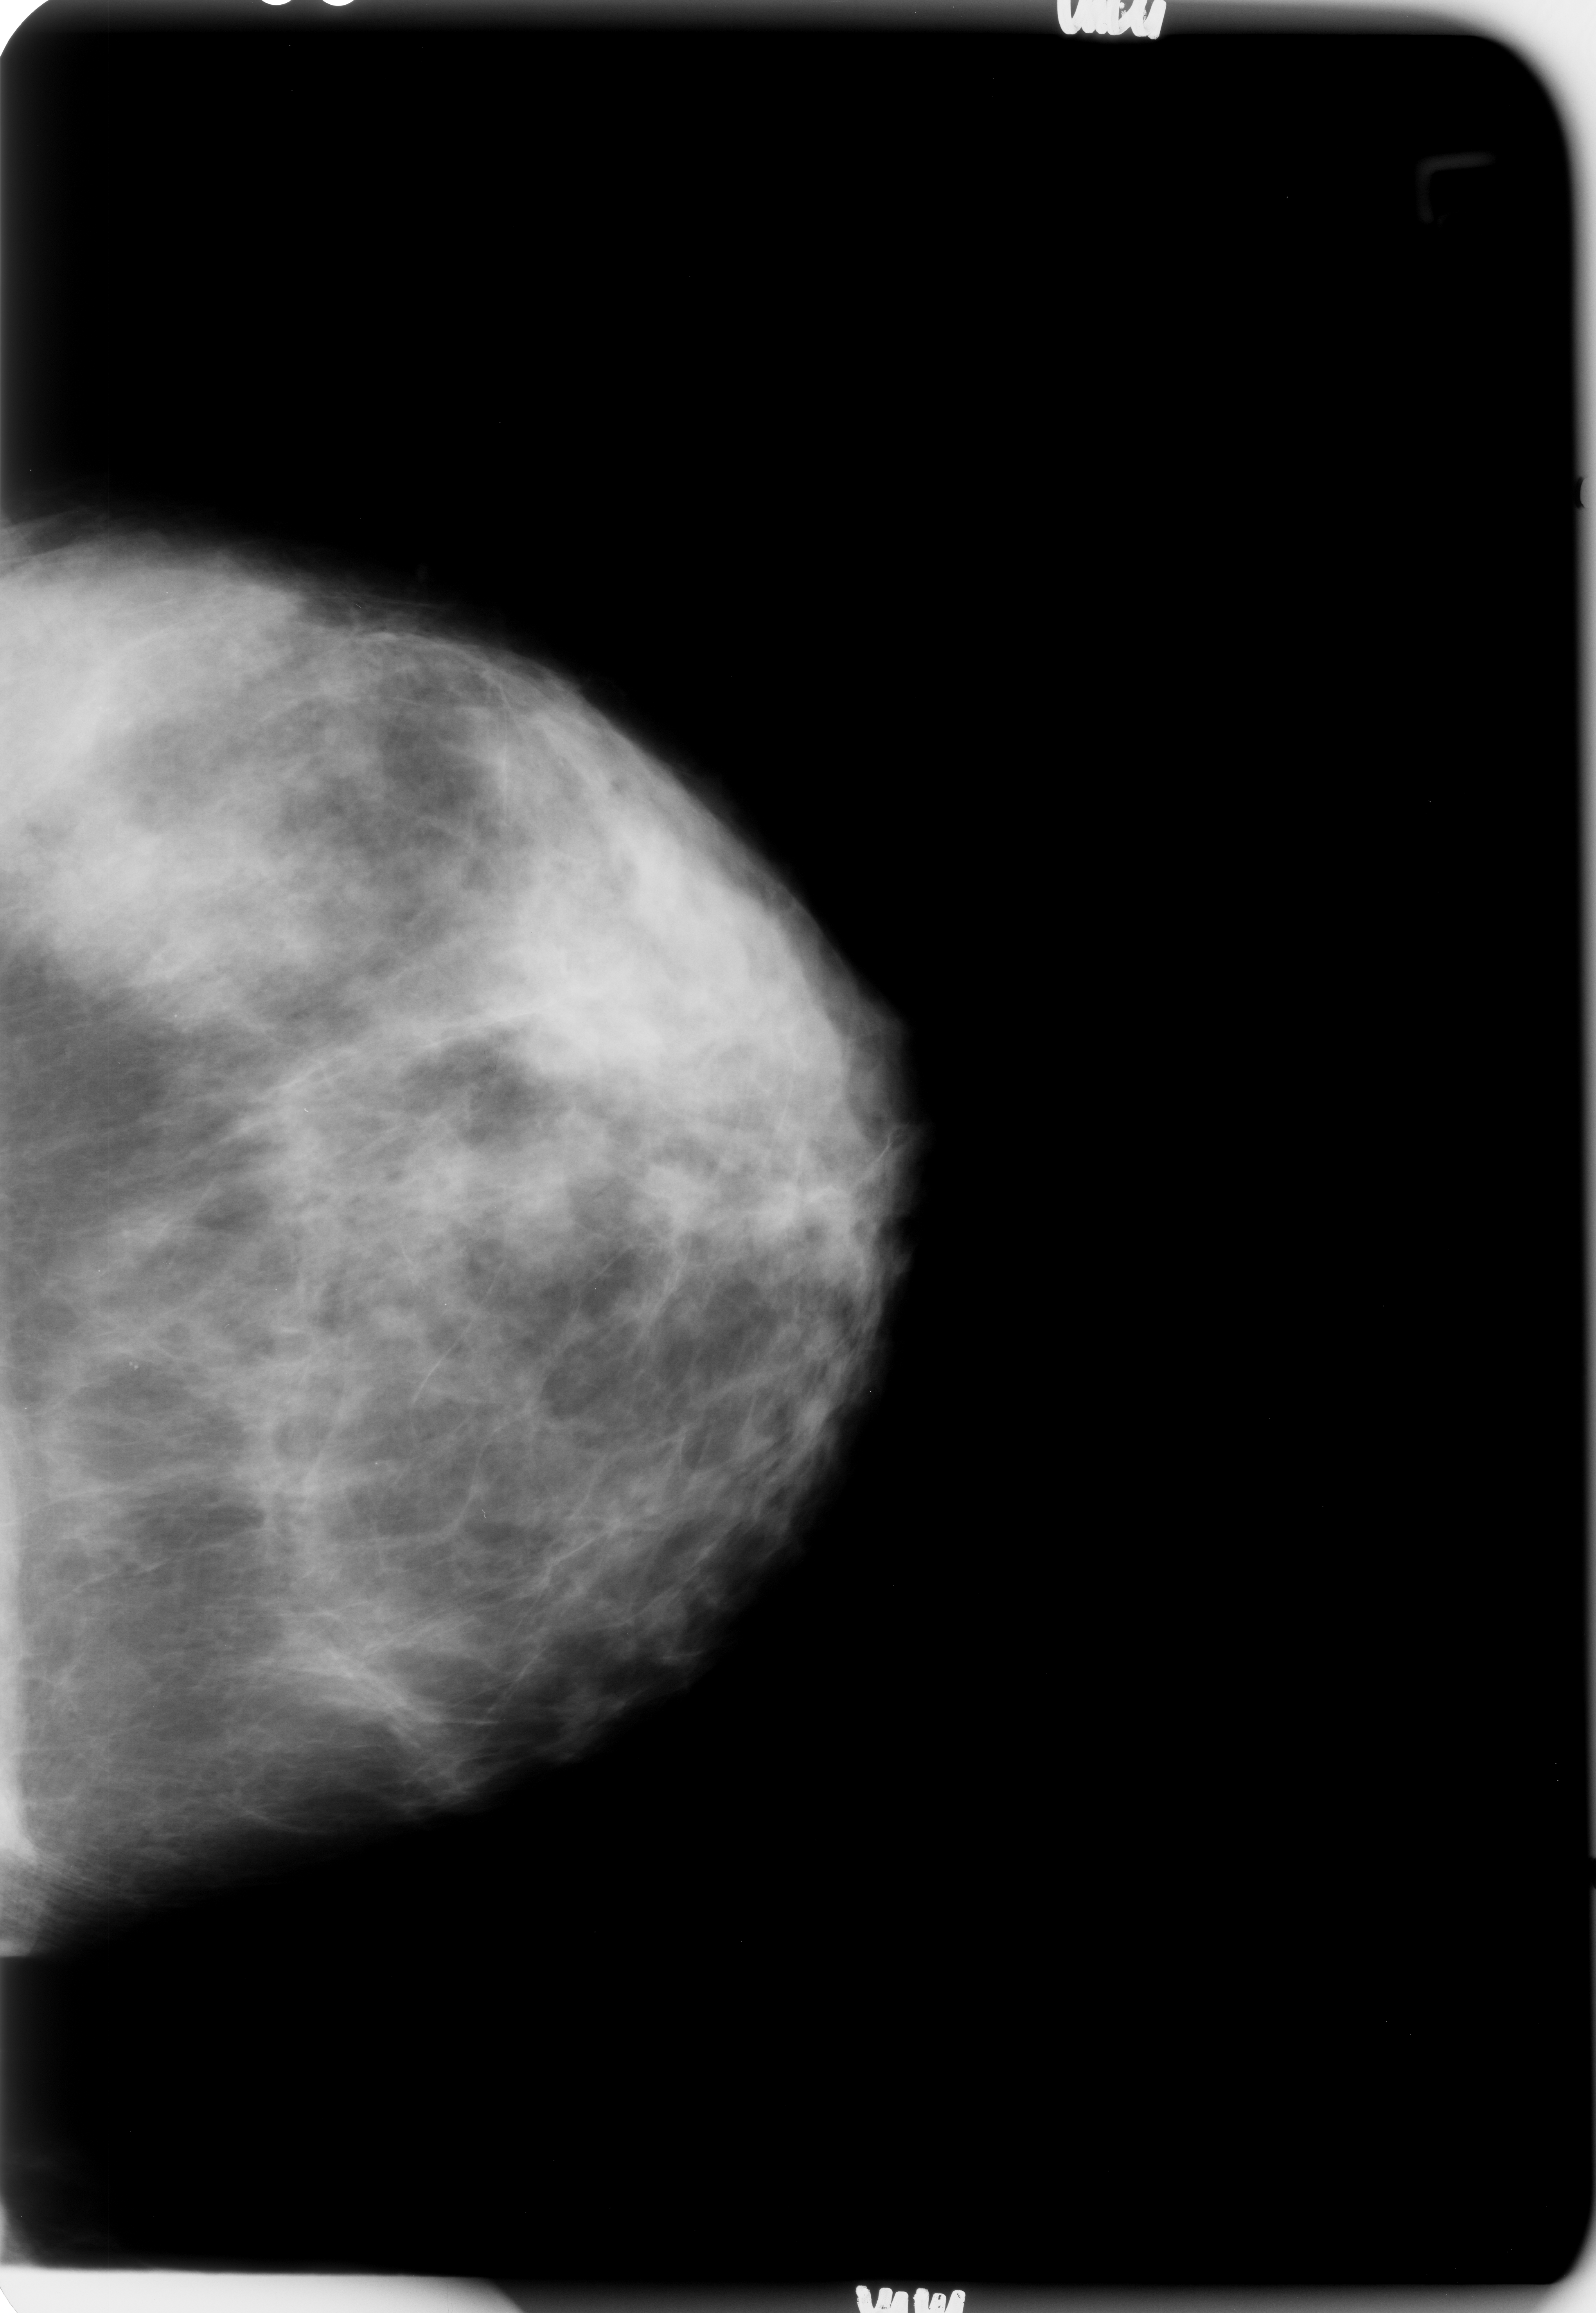
Digitized screen-film mammogram, left breast, CC view, BI-RADS breast density category 3 (scale 1–4).
Marked findings (only marked abnormalities are described; nothing is implied about the rest of the image): calcifications, morphology amorphous / pleomorphic, distribution clustered; BI-RADS assessment category 4; subtlety rating 2 on a 1 (subtle) to 5 (obvious) scale; pathology result (as recorded, not read from the image): malignant.